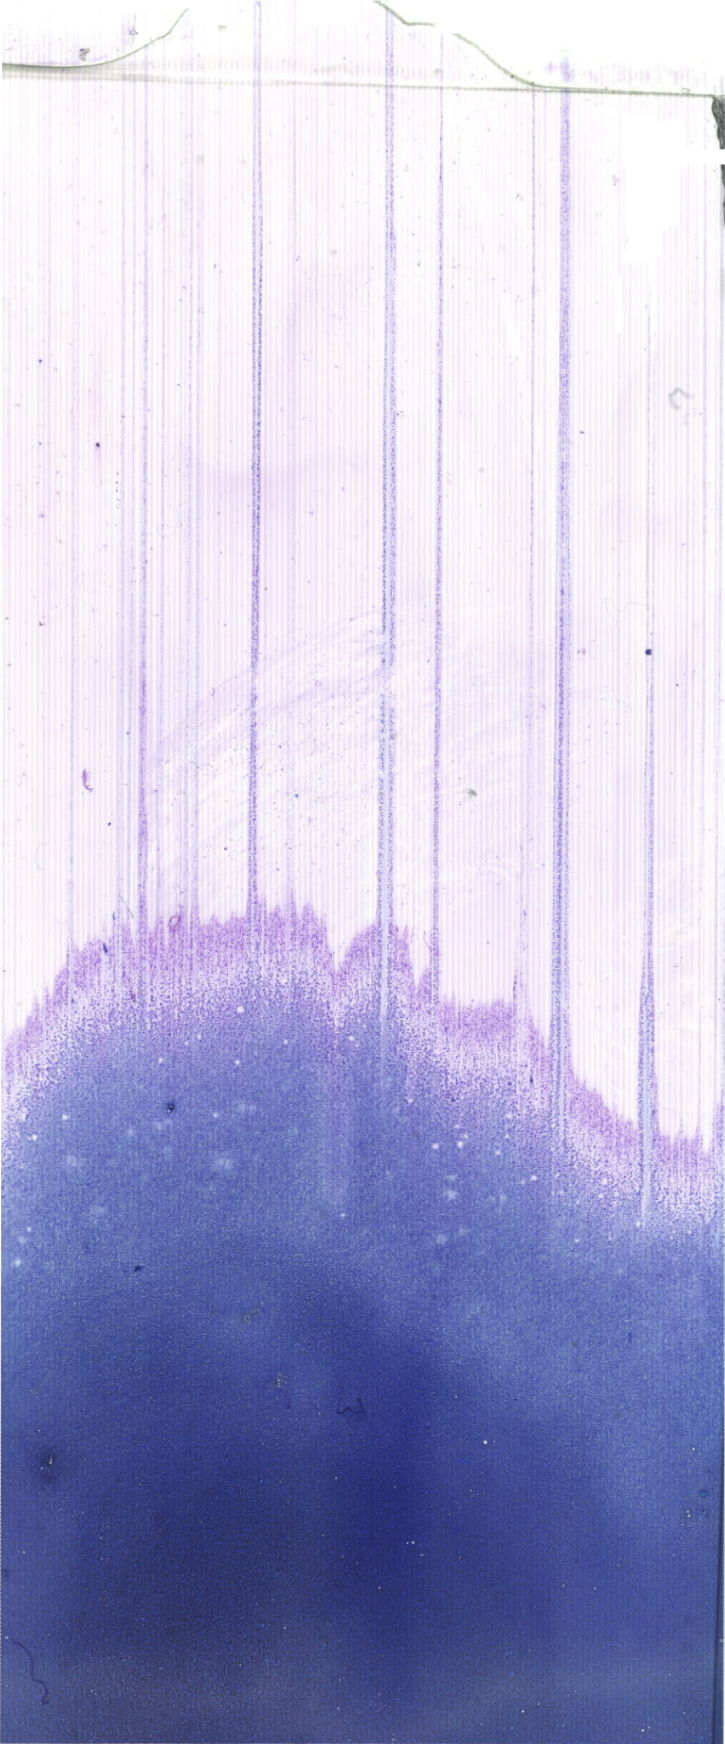
Whole-slide image of a May-Grünwald-Giemsa (MGG)-stained bone marrow aspirate smear, shown as a low-resolution overview of the whole scanned area (about 20.6 x 49.4 mm). Patient sex: male.
Diagnosis: Acute Erythroid Leukemia.